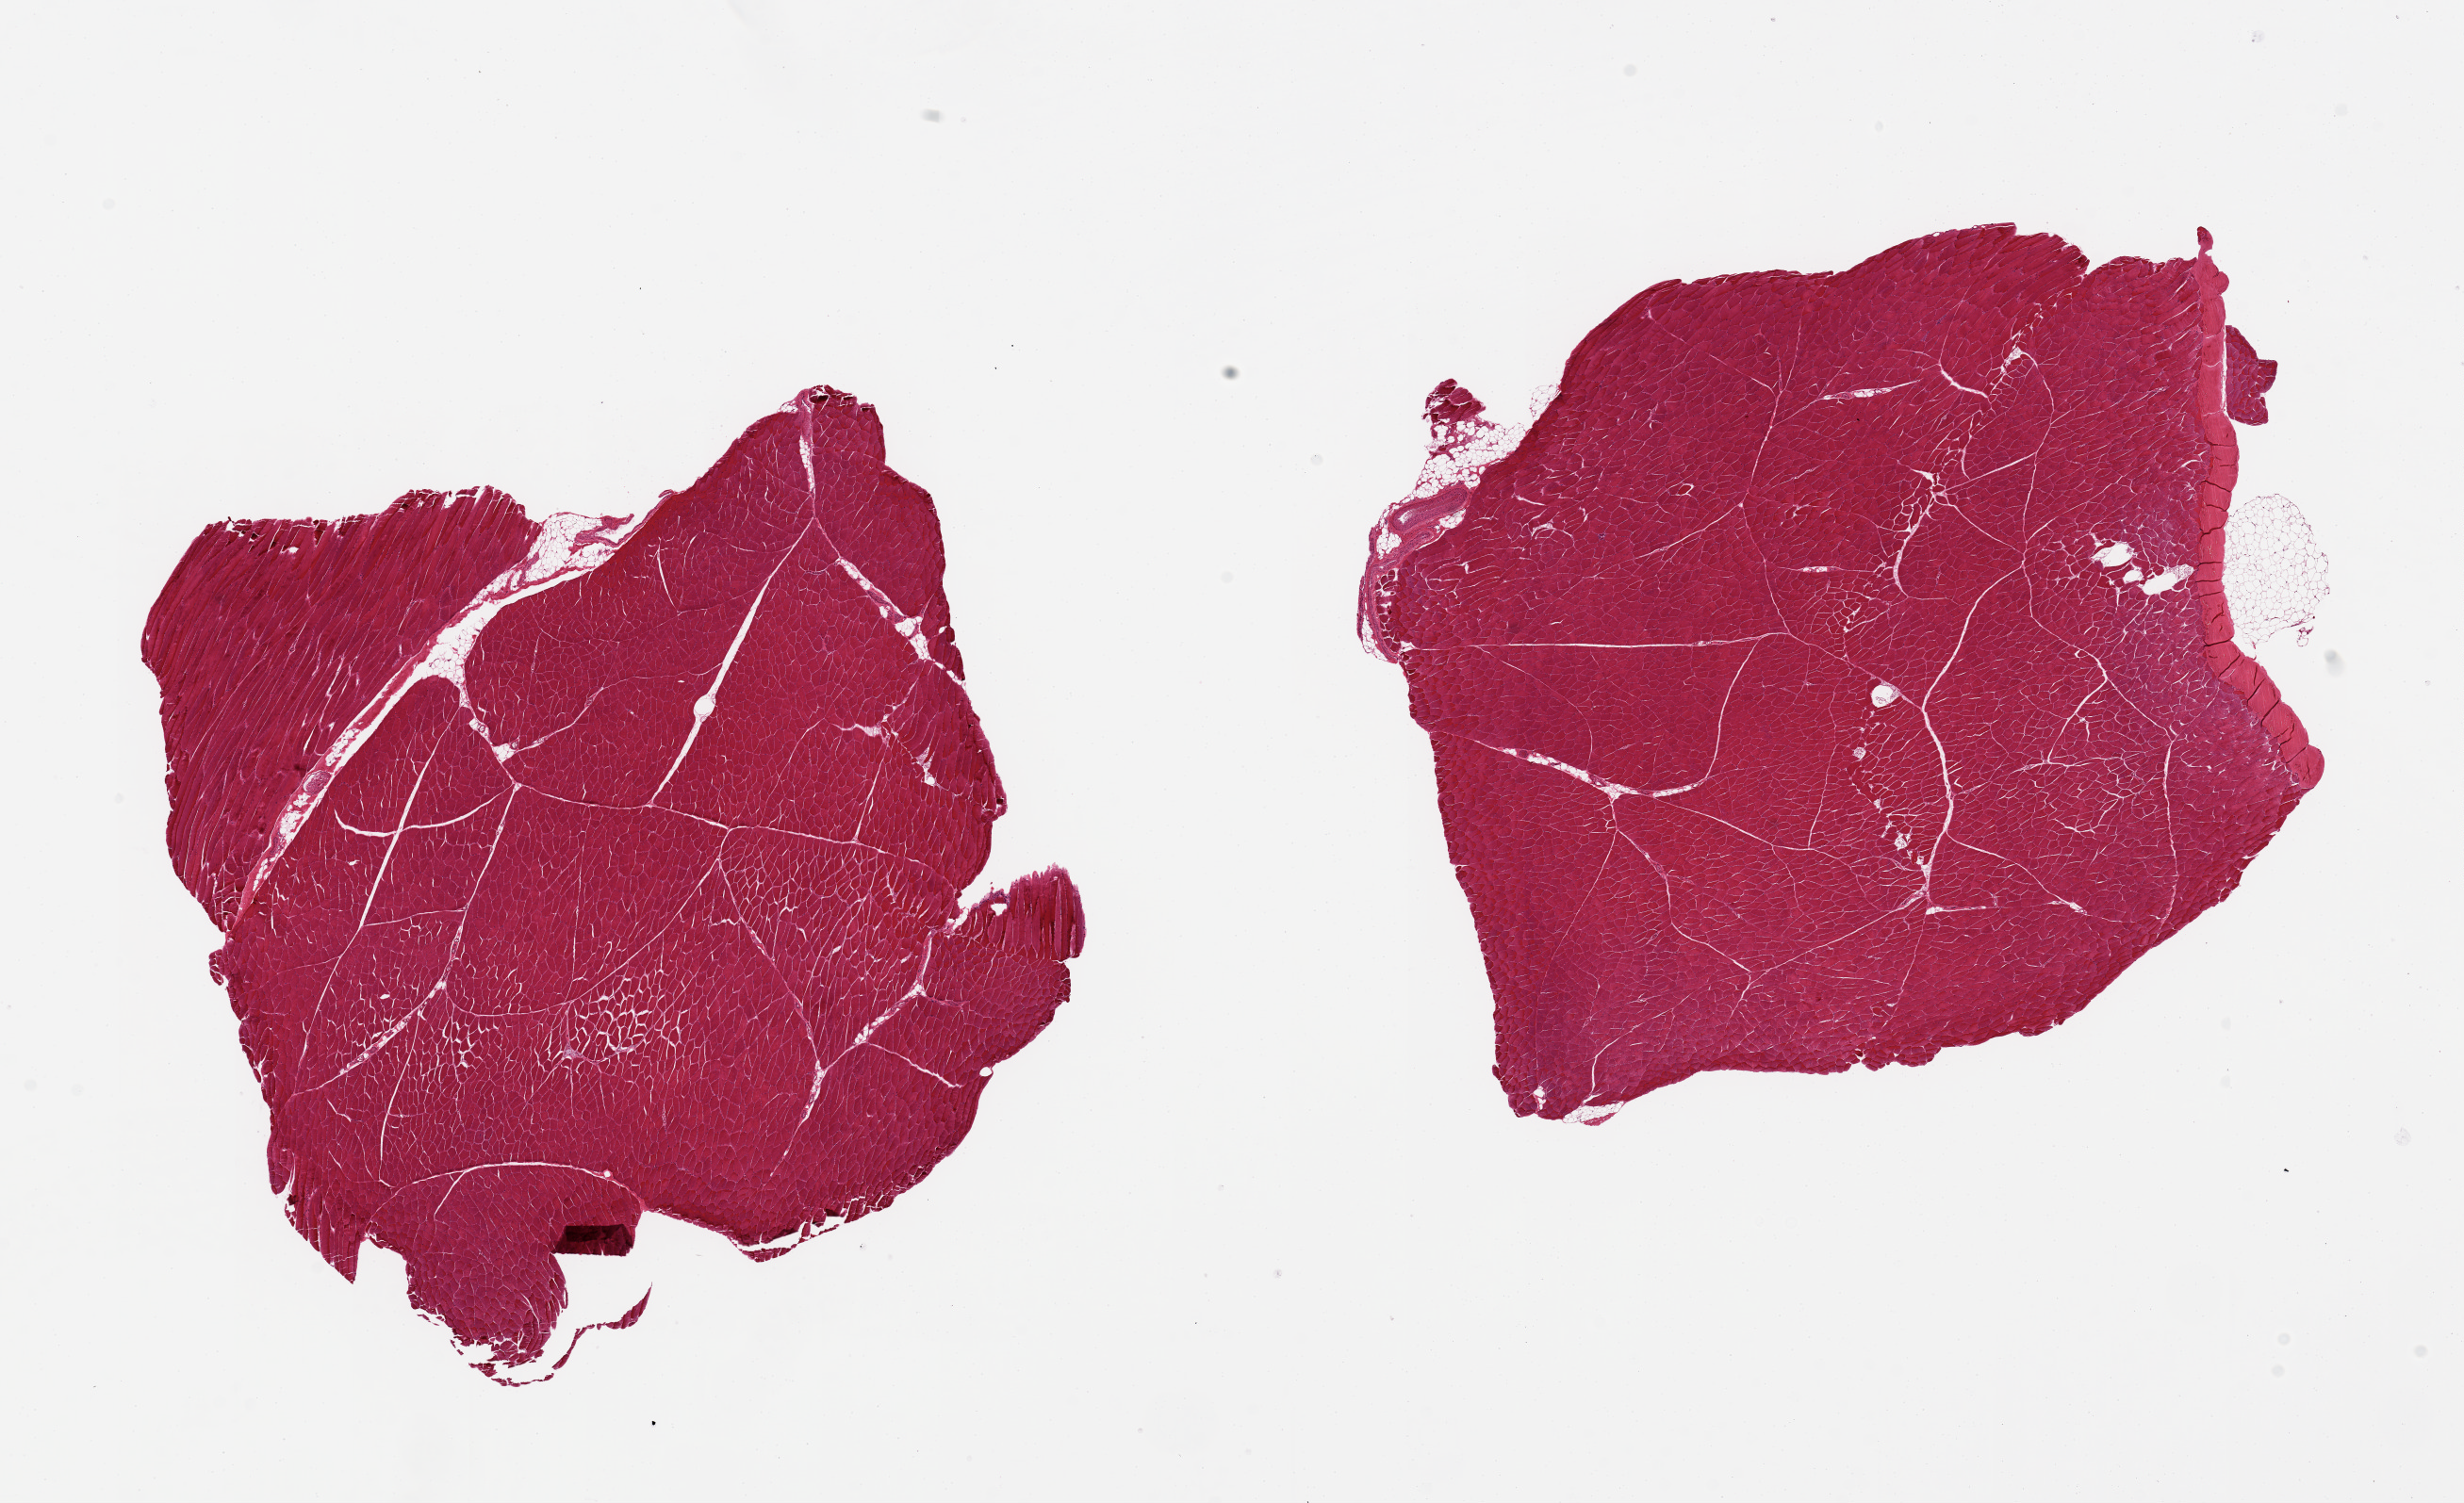
Whole-slide image, hematoxylin and eosin (H&E) stain — whole scanned area (about 20.7 x 12.6 mm, slide scanned at 20x) shown as a low-resolution overview. PAXgene-fixed, paraffin-embedded tissue. Section of skeletal muscle (target tissue). Donor tissue sample. Male donor.
Reviewer comment on this tissue sample: 2 pieces, 8x7 & 8x7mm; minimal interstitial fat, good aliquots.